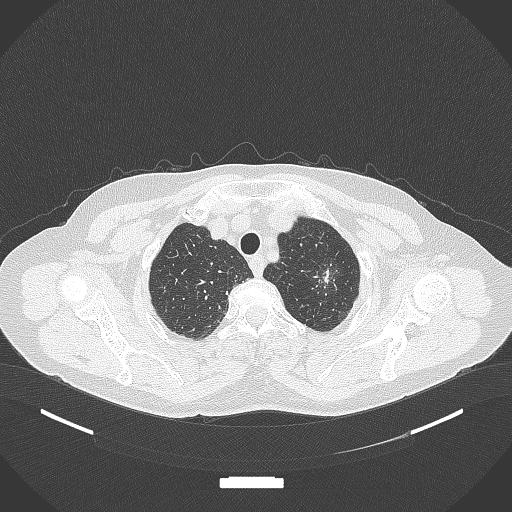
Chest CT, one axial slice; reconstruction kernel B70f; 120 kVp; lung window (W 1500 / L -600 HU); 512 × 512 image matrix, field of view 400 × 400 mm. Patient: female, 64 years. Case-level facts recorded for this patient, not image findings: clinical TNM (as recorded): T1c N0 M0; histopathological grade: G1.
Annotated regions visible in this slice (bounding box drawn by a radiologist):
- lung tumour (recorded histology: adenocarcinoma): bounding box [x1, y1, x2, y2] px = [310, 255, 341, 301]